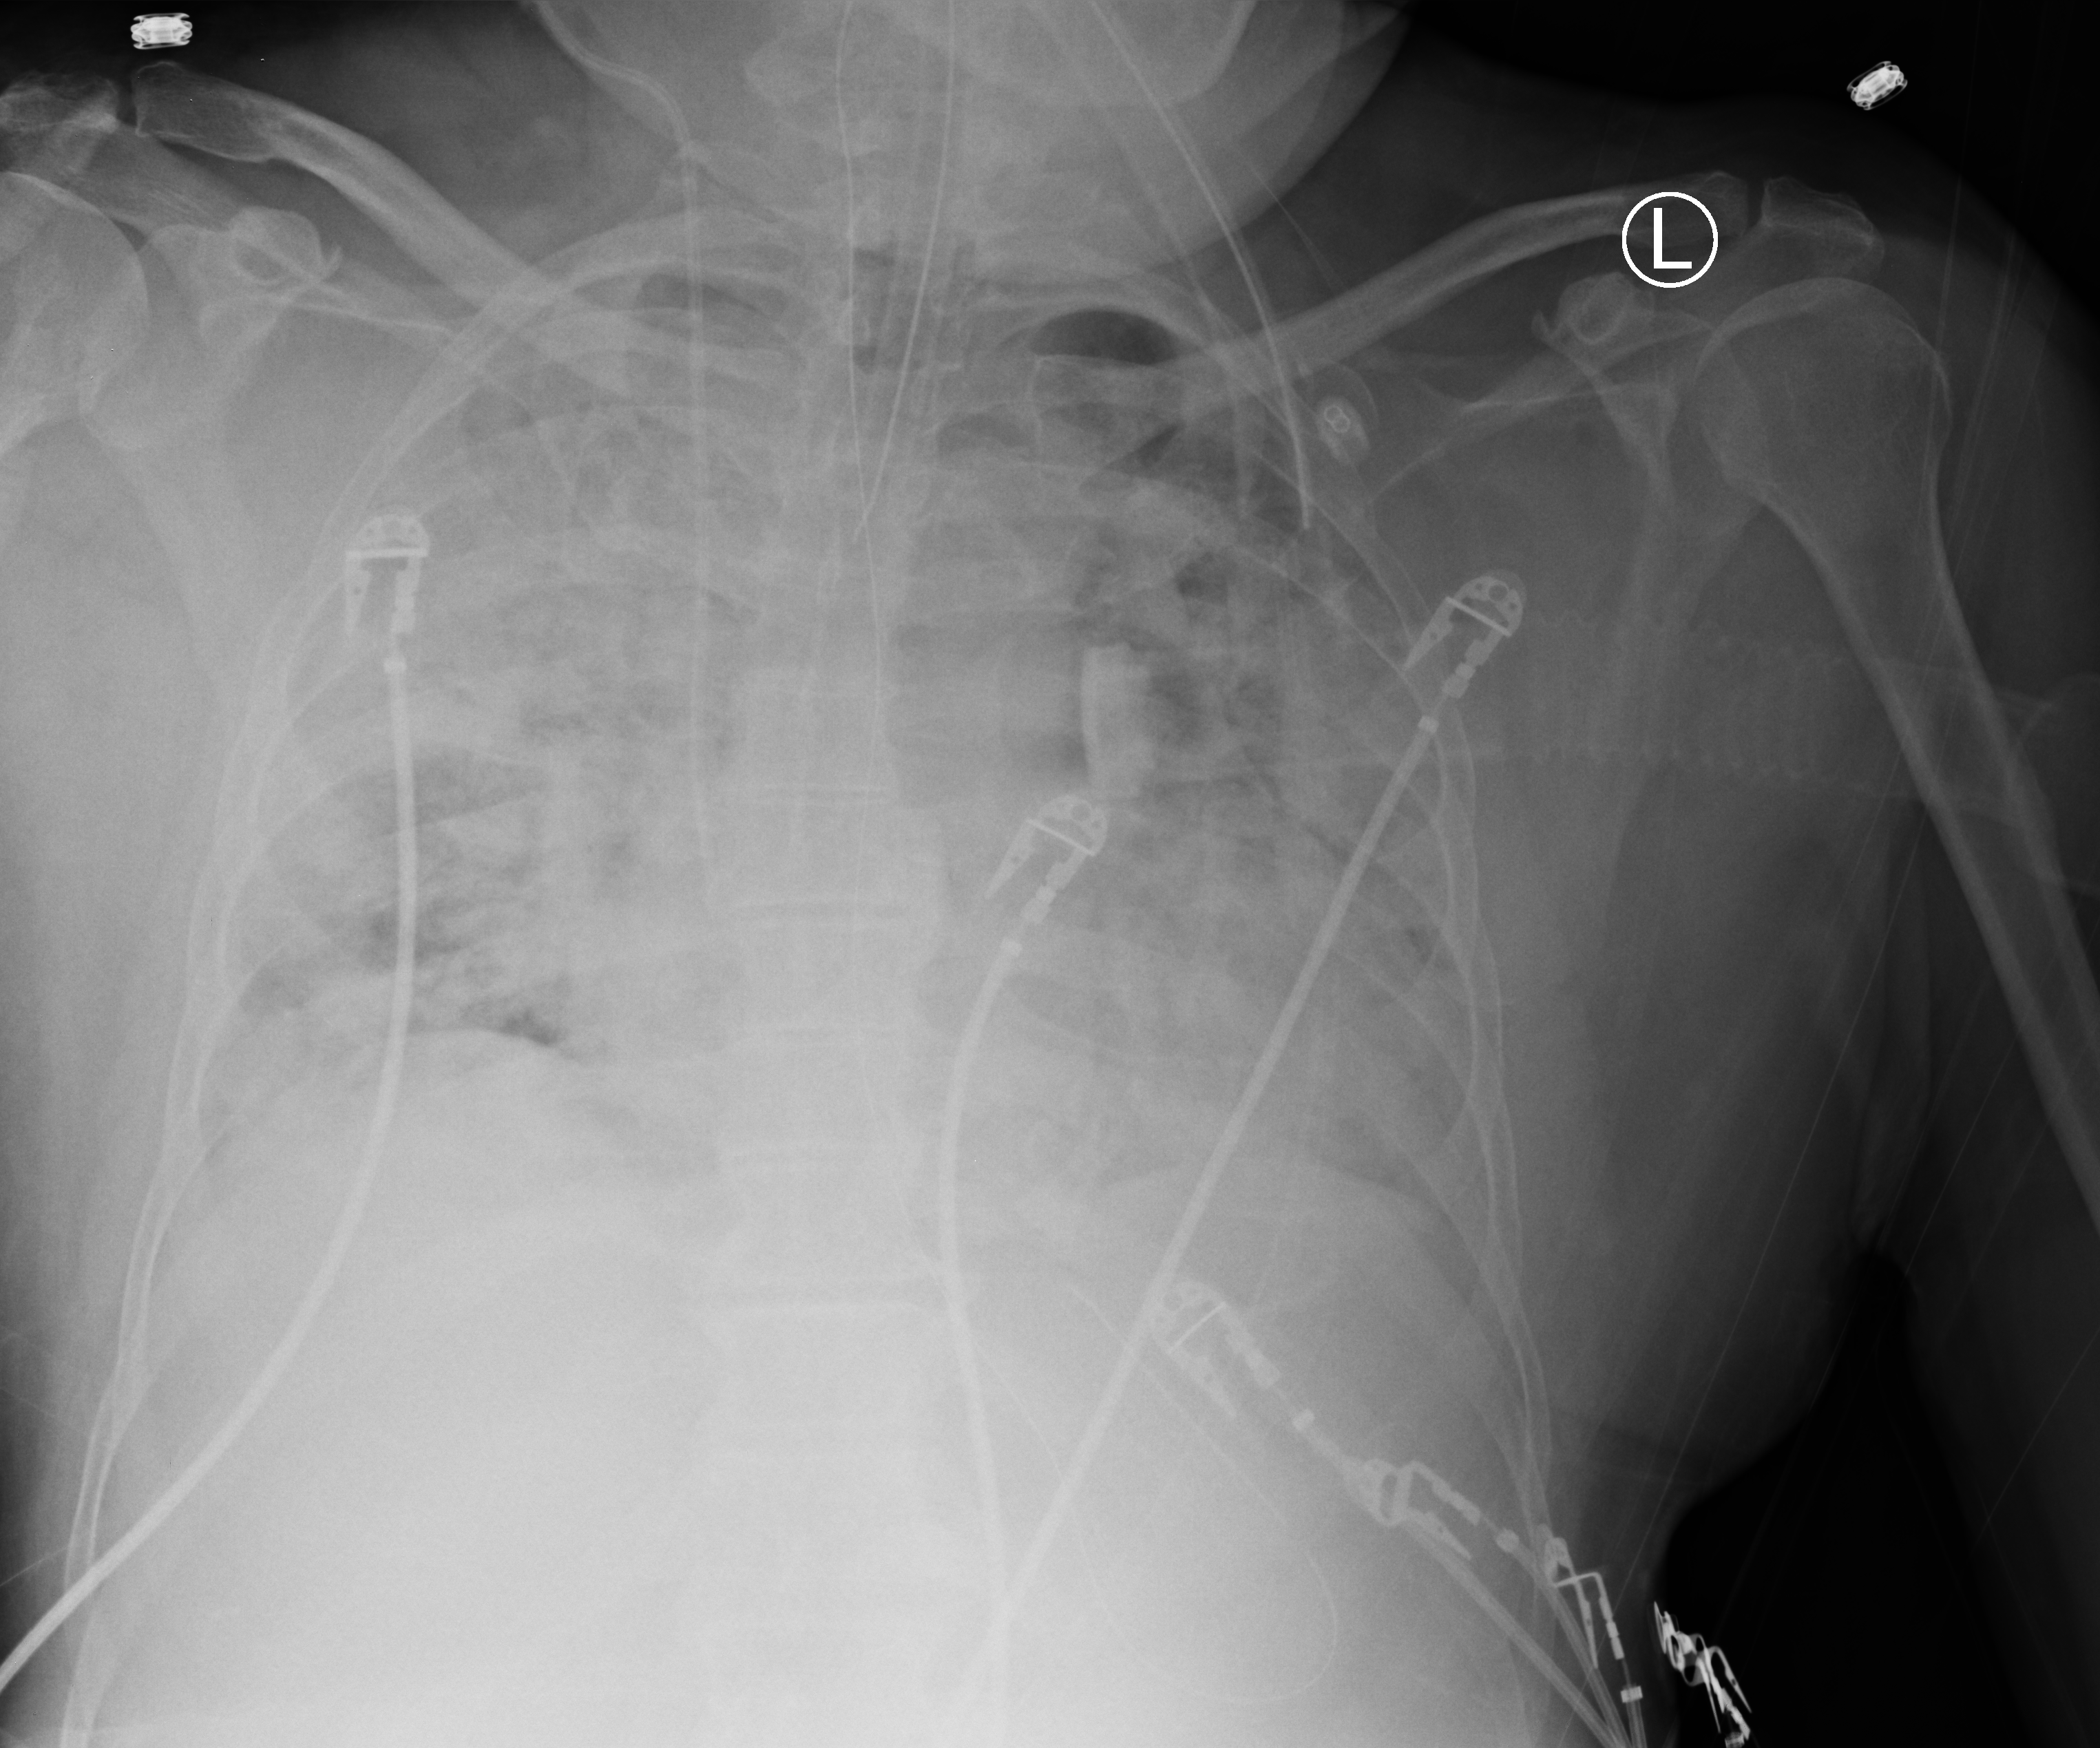
Chest X-ray (portable), anteroposterior (AP) projection. Patient hospitalised with COVID-19; male, aged 60–74 years.
From the hospital-stay record, not from the radiograph (when in the stay this image was taken is not recorded): length of hospital stay: 31 days; mechanically ventilated during this hospital stay: yes; chronic kidney disease (admission record): no.